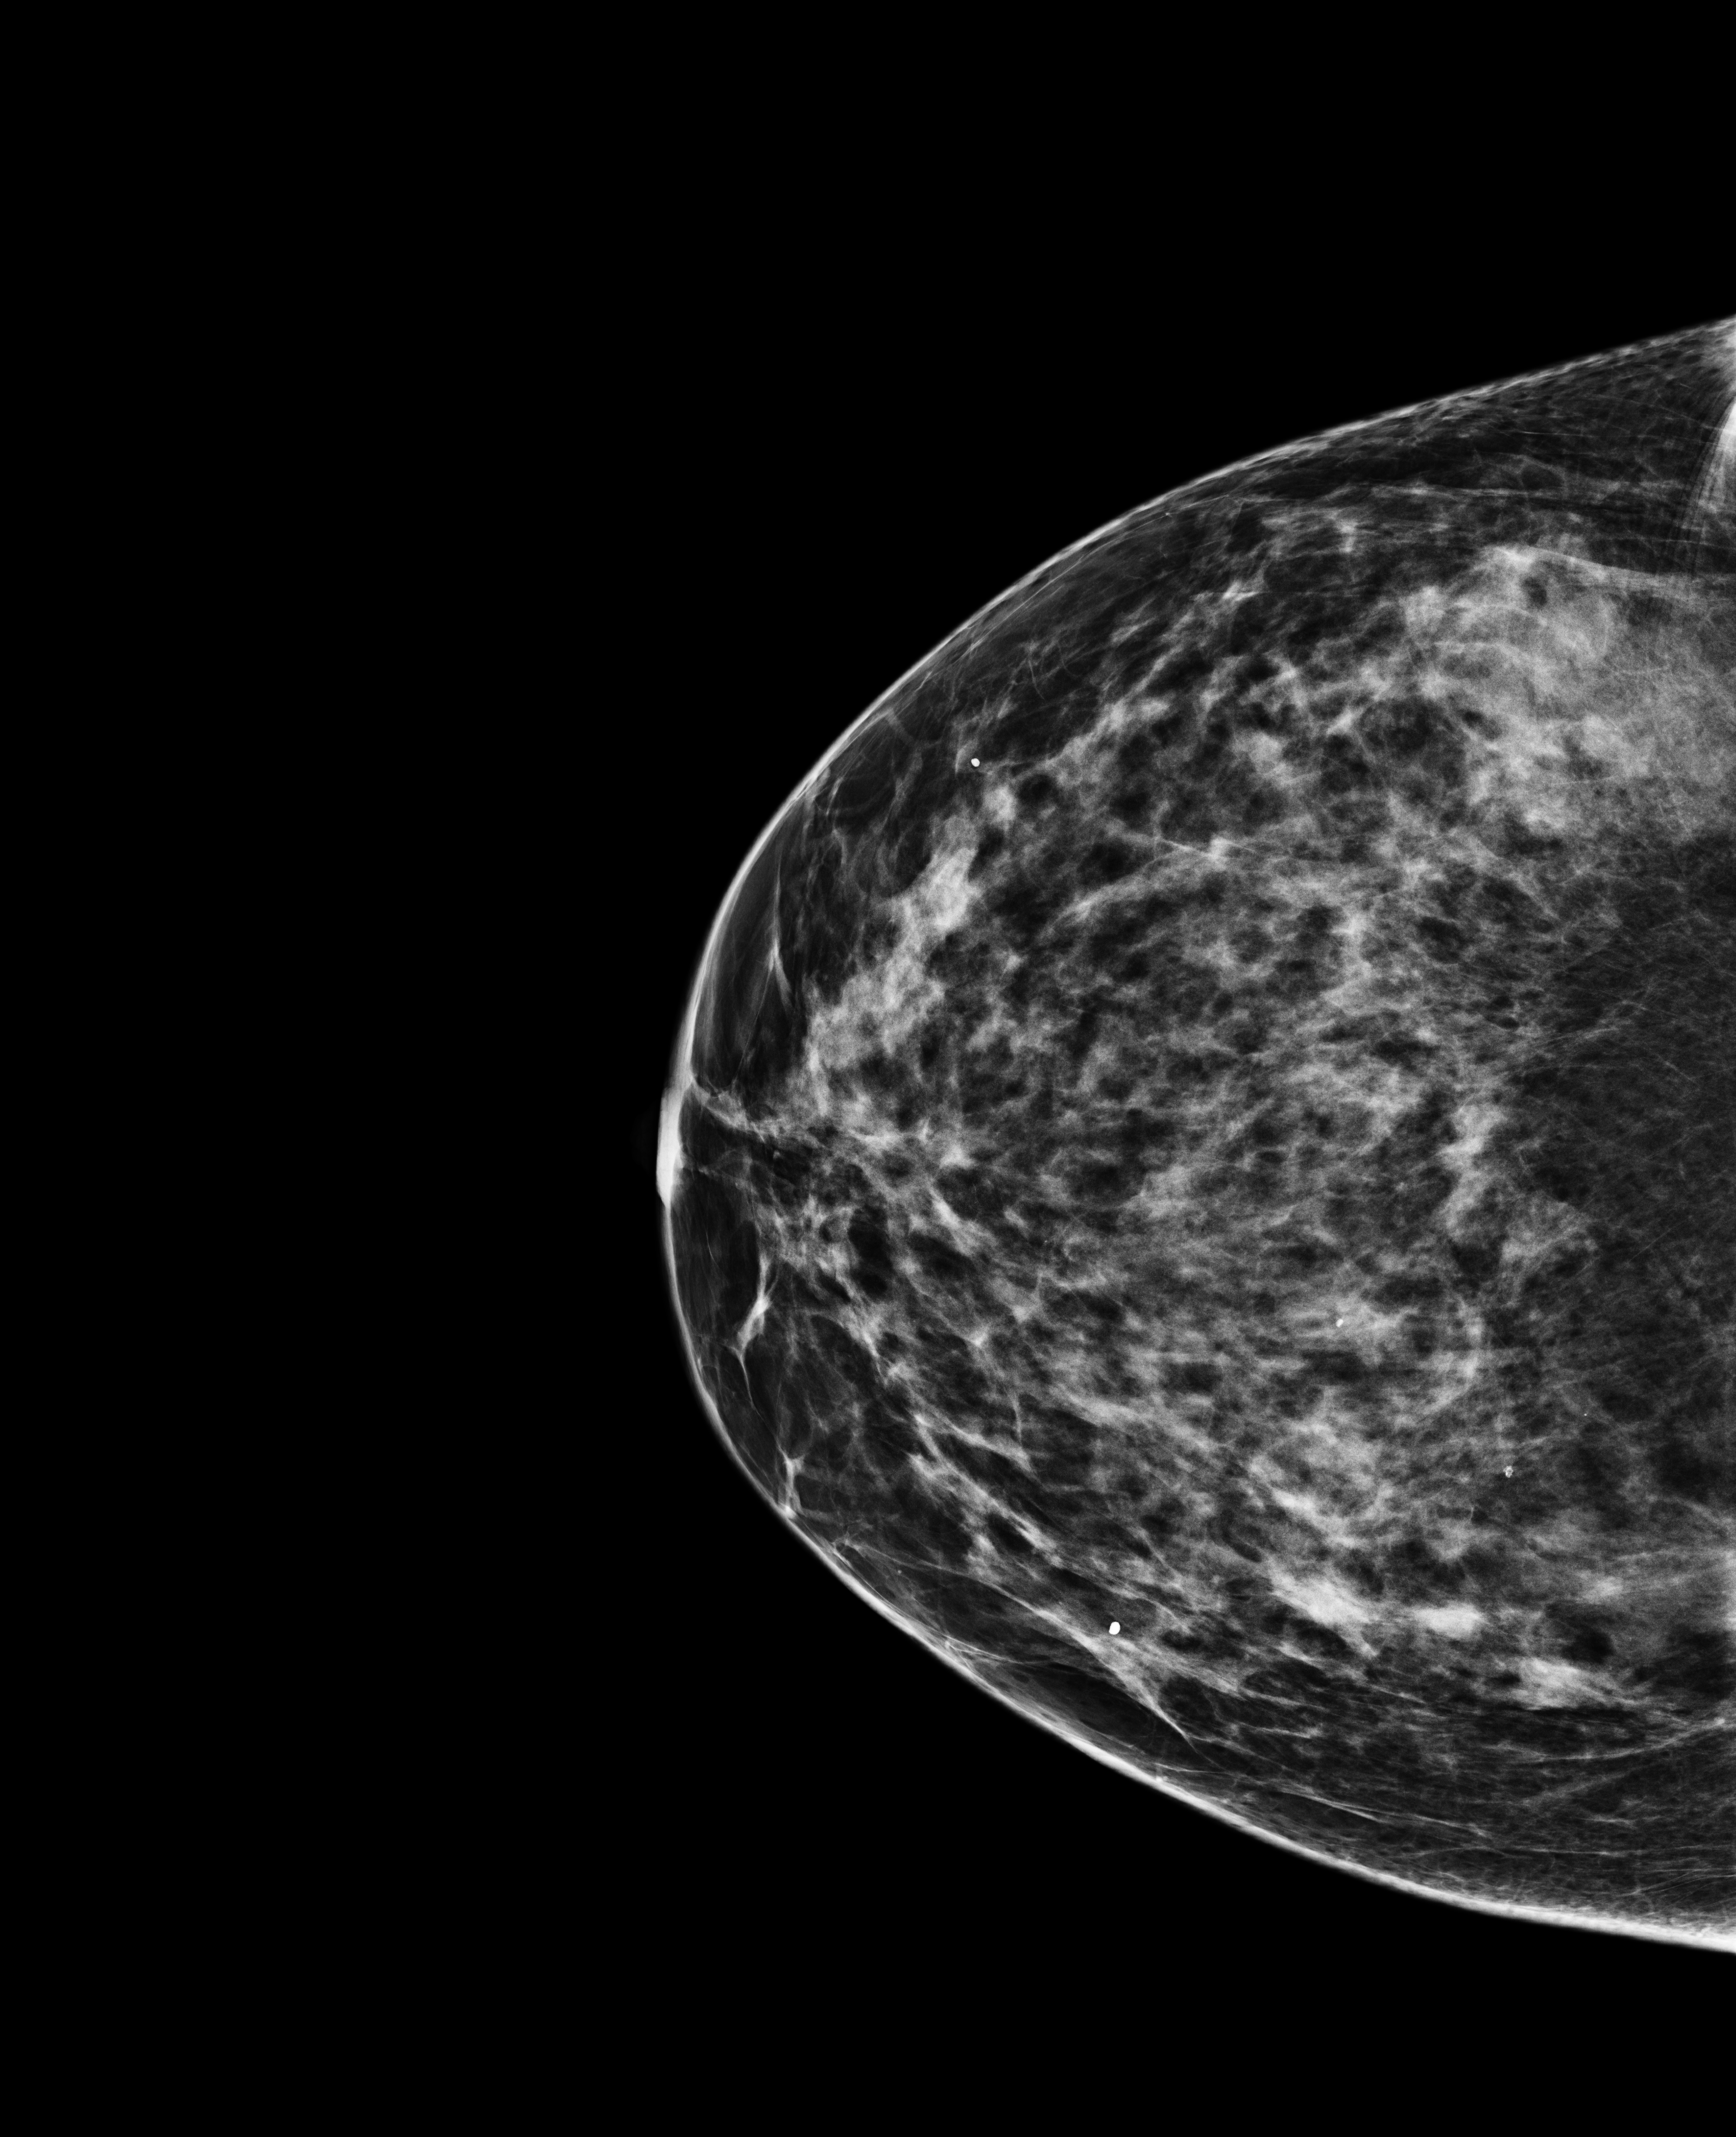
Full-field digital mammogram (FFDM), right breast, cranio-caudal projection, screening examination. Patient: female, 44 years.
Breast density at the screening exam (both breasts): heterogeneously dense (BI-RADS density category c). Final BI-RADS category for the screening round (tomosynthesis exam, both breasts): category 2. Recall: no recall after this screen.